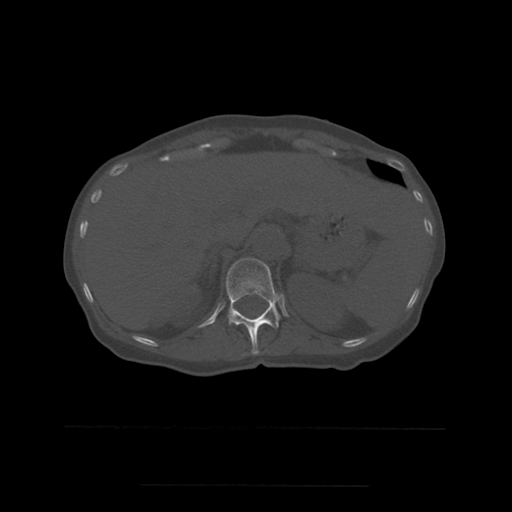
CT including the spine, one axial slice. Slice 258 of 544 in the series (ordered by position). Bone window (W 1800 / L 400 HU). 1.25 mm slice thickness. 512 × 512 image matrix. Patient age 58 years. From the clinical record (not read from this slice): primary cancer: lung.
Annotated regions visible in this slice (semi-automatic segmentation, software-assisted and operator-edited):
- T12 vertebra: box from (x=226, y=258) to (x=280, y=355) px